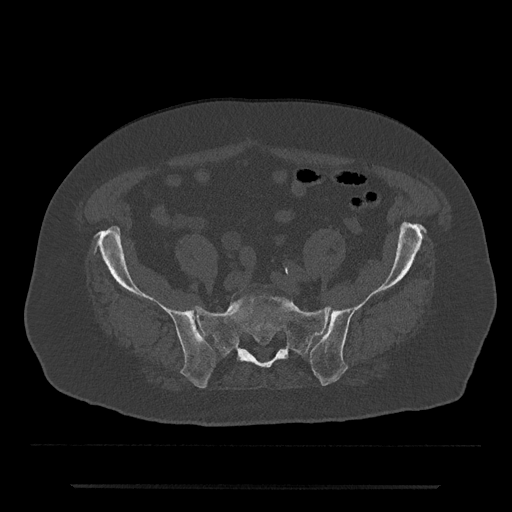
CT including the spine, one axial slice. Slice 230 of 797 in the series (ordered by position). Reconstruction kernel Br40s/3. 120 kVp. Bone window (W 1800 / L 400 HU). 0.5 mm slice thickness. 512 × 512 image matrix, field of view 434 × 434 mm. Patient: male, 80 years. From the clinical record (not read from this slice): primary cancer: prostate; vertebrae with lytic lesions (as recorded): L1, T11.
Annotated regions visible in this slice (semi-automatic segmentation, software-assisted and operator-edited):
- L5 vertebra: bounding box (x1, y1, x2, y2) in pixels: (240, 294, 265, 300)